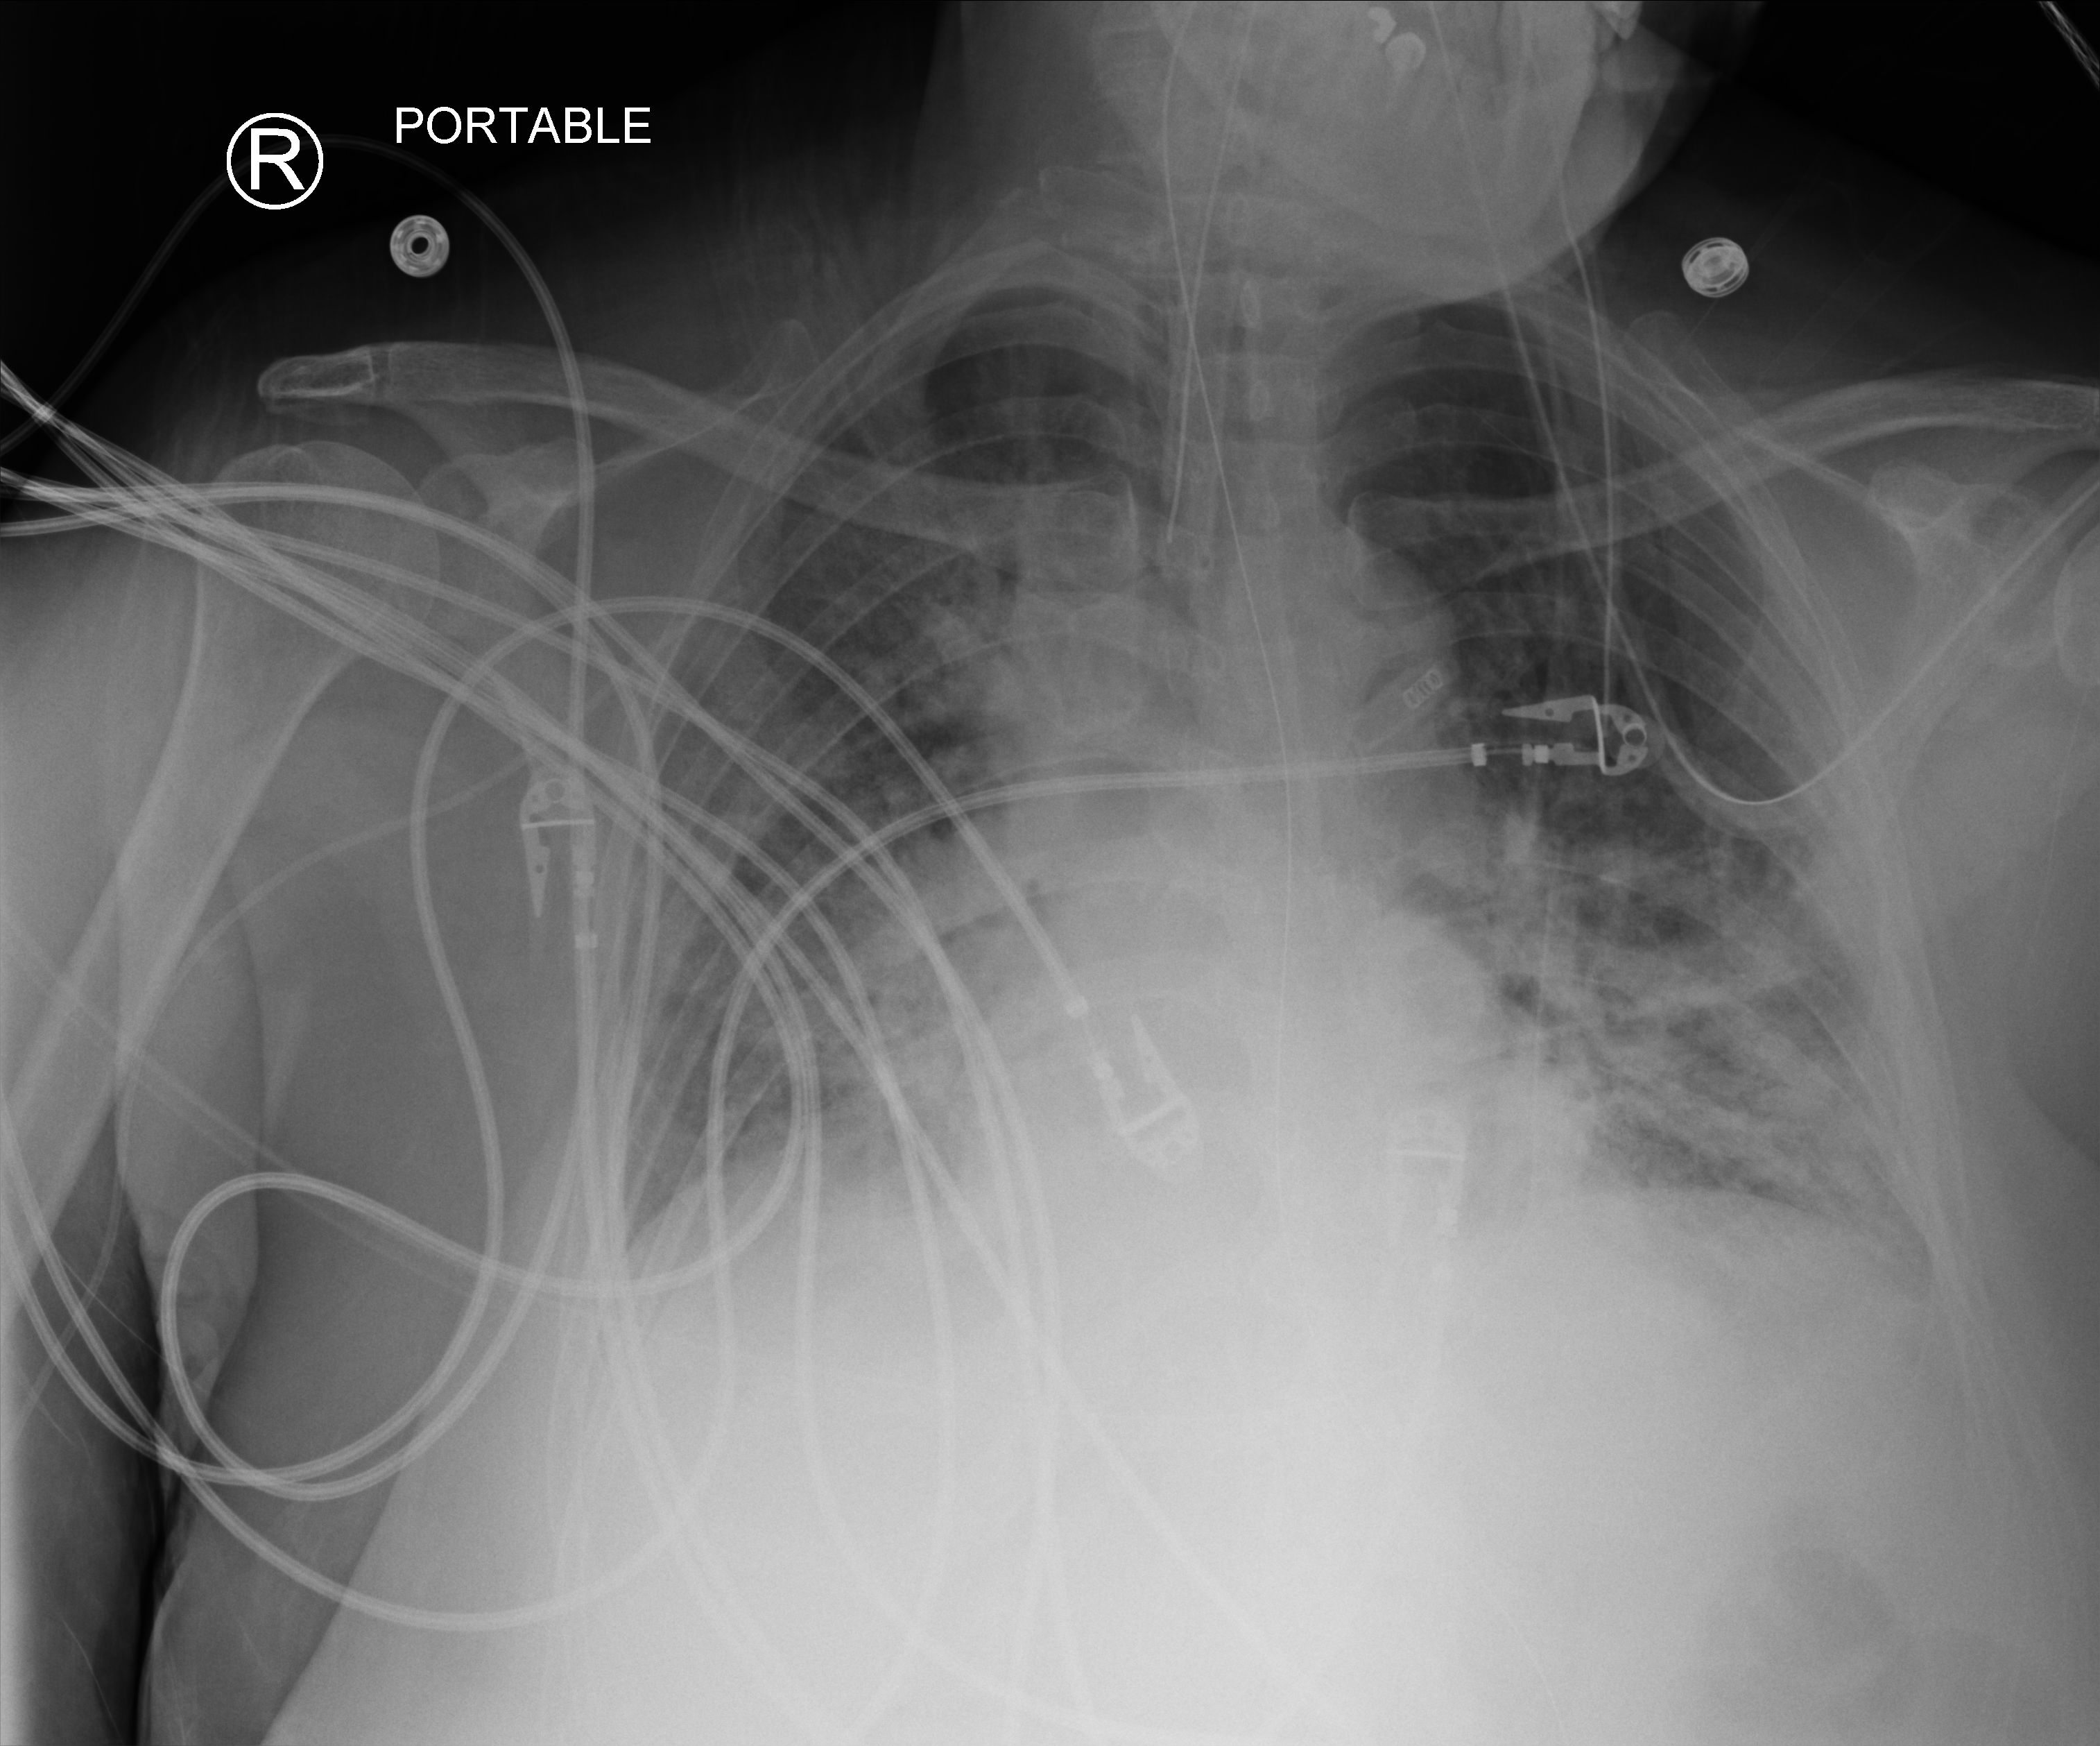
Bedside chest radiograph (computed radiography), anteroposterior (AP) projection. Female patient hospitalised with COVID-19, age 18–59 years.
Hospital-stay facts (about this admission, not read from this image; timing relative to this image not recorded): other chronic lung disease (admission record): no.